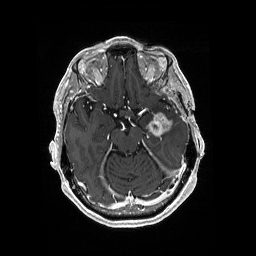
Brain MRI from a brain-tumour surgery series, one axial slice; position 116 of 176 along the scan axis; T1-weighted post-contrast; 256 × 256 image matrix, field of view 256 × 256 mm. From the clinical record (not read from this slice): histopathology: Glioblastoma; WHO grade: 4; IDH mutation: no; tumour location: Left Medial Temporal.
Outlined on this slice (outlined manually by an expert reader):
- tumour: bounding box [x1, y1, x2, y2] px = [146, 111, 174, 137]